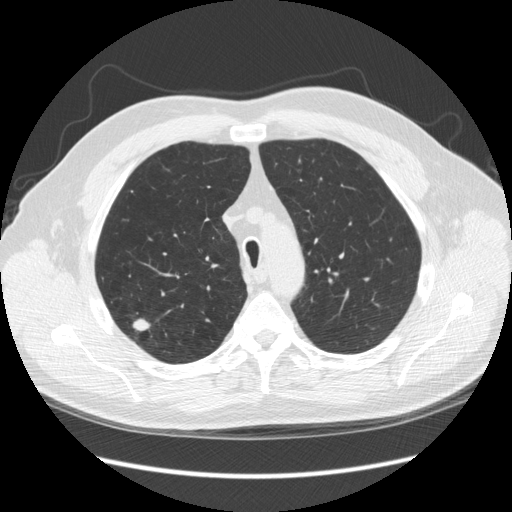
Low-dose screening chest CT, one axial slice. Position 190 of 248 along the scan axis. Reconstruction kernel STANDARD. Lung window (W 1500 / L -600 HU). 512 × 512 image matrix.
Annotated regions visible in this slice (manually delineated by an expert):
- lesion 1 (tumor, upper lobe of right lung): bounding box <133,318,150,331> (left, top, right, bottom; pixels)